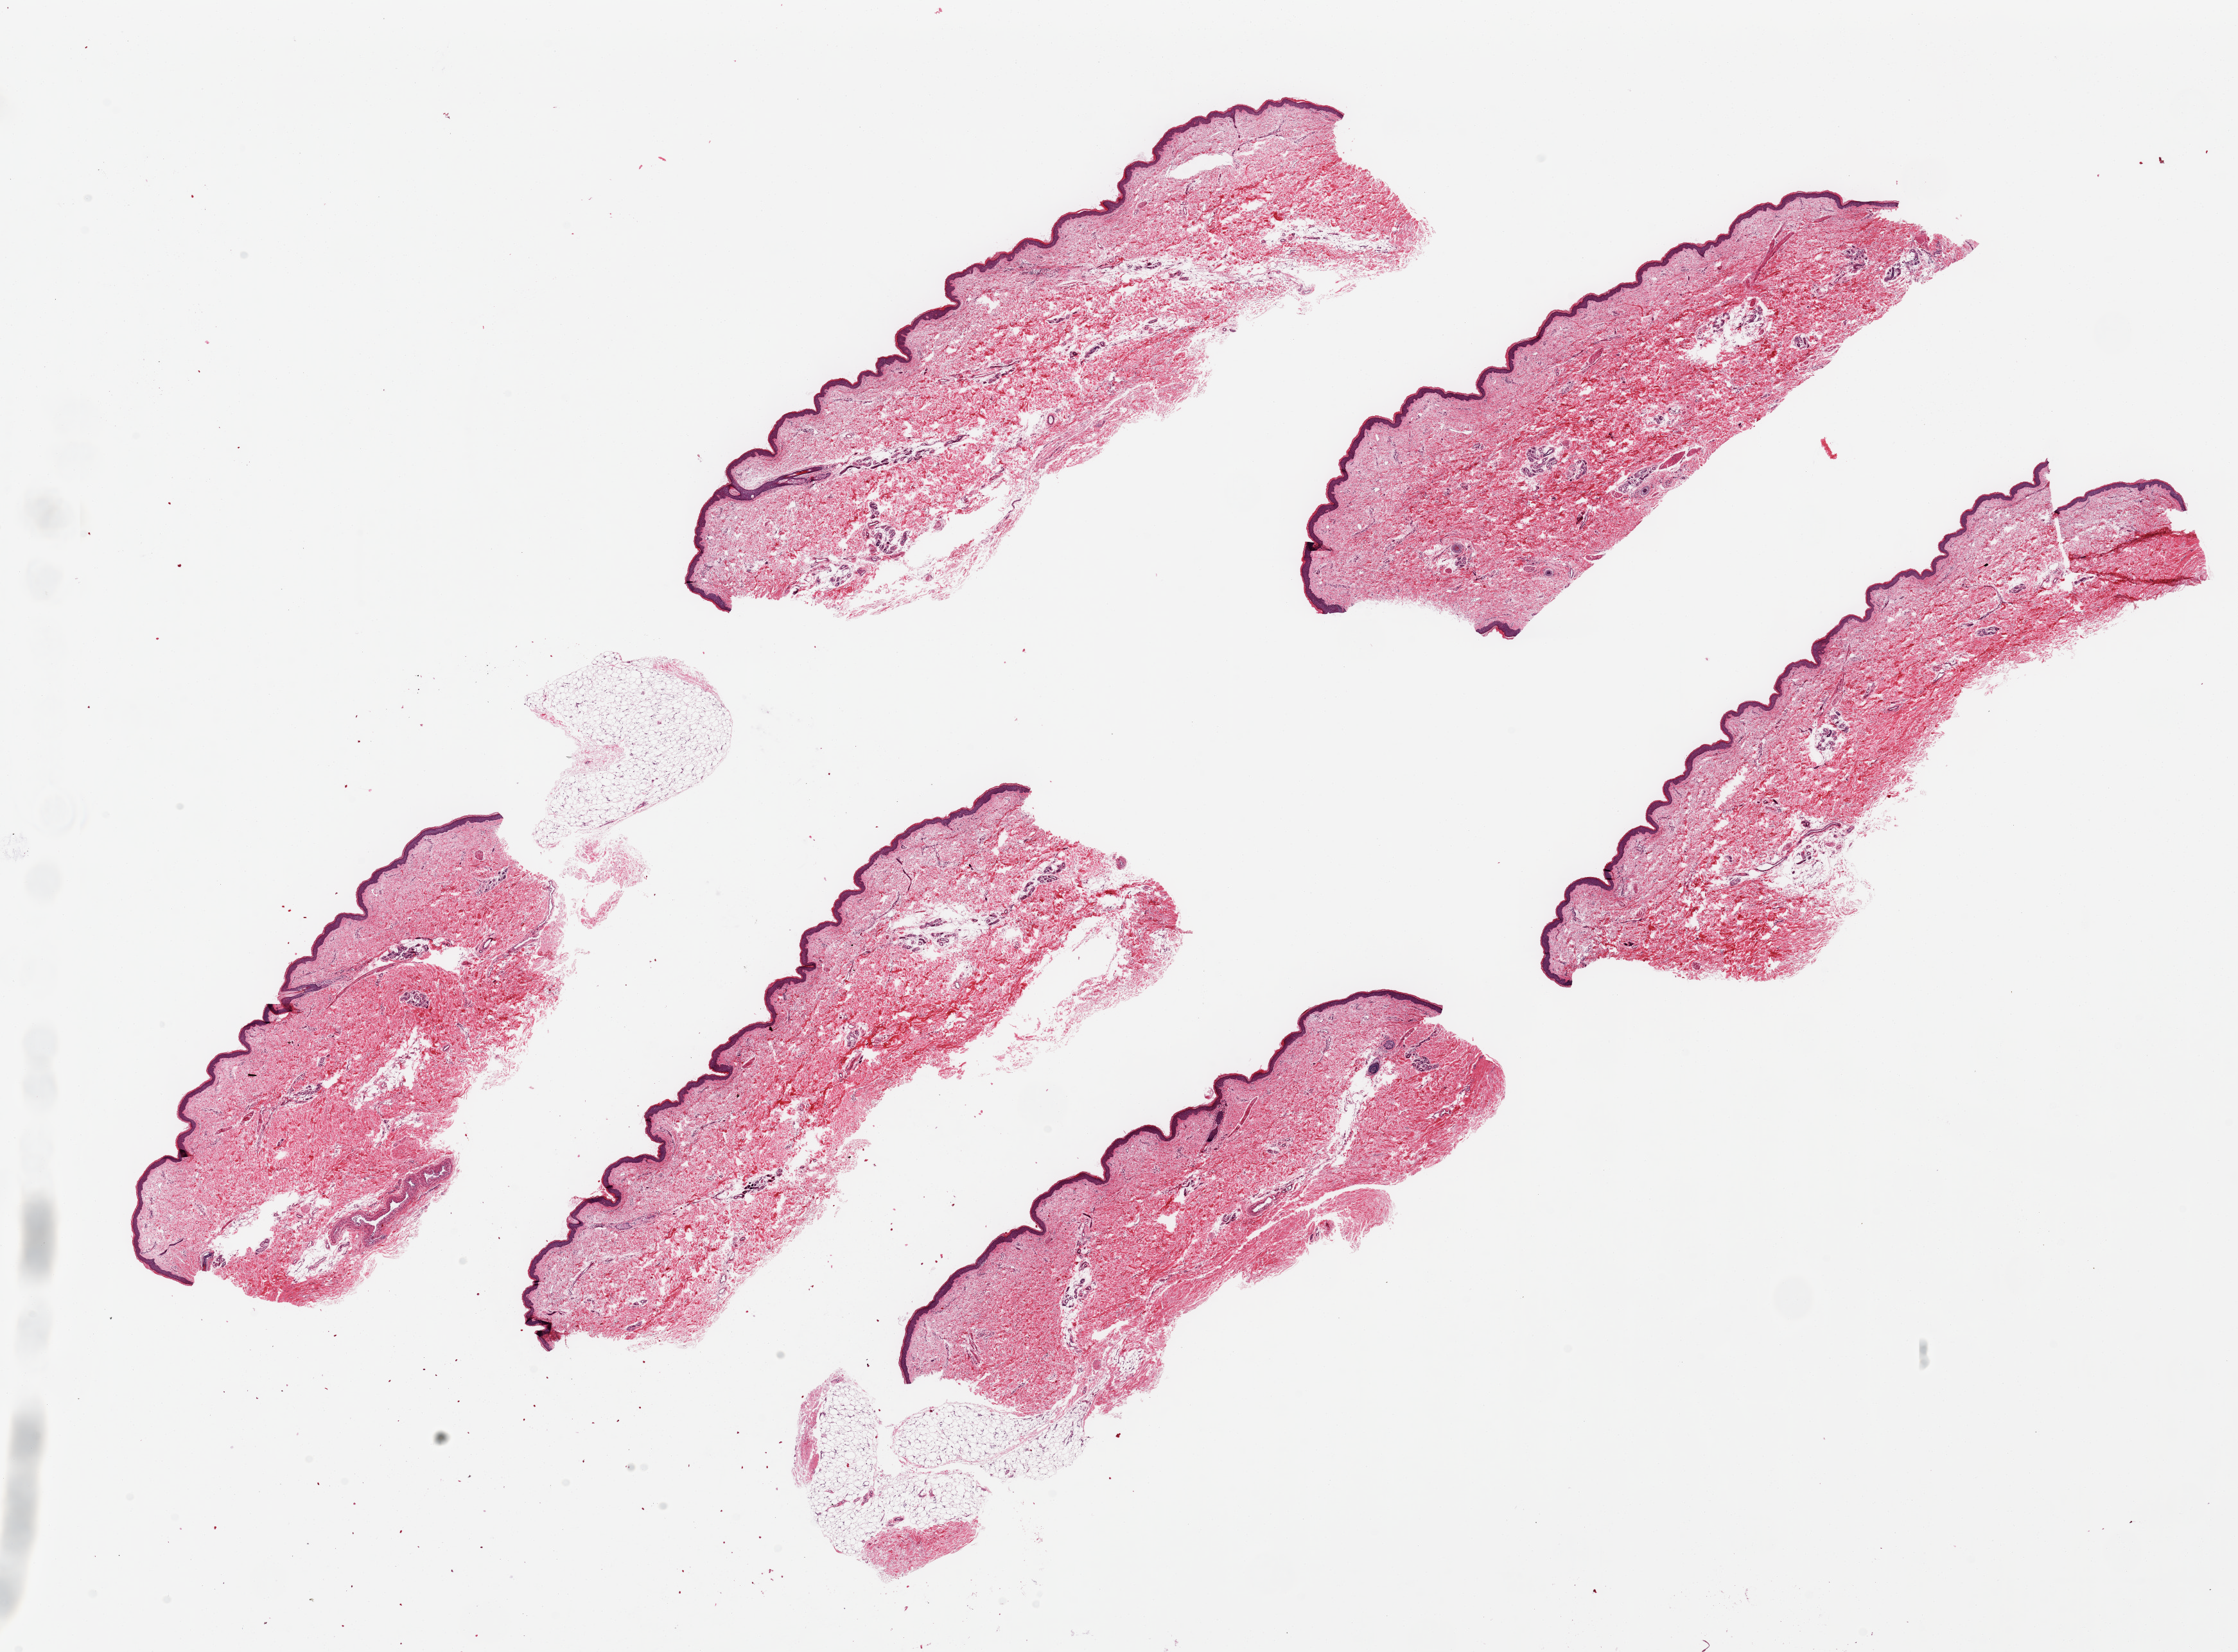
Whole-slide image, haematoxylin and eosin stain — low-resolution overview of the scanned area, about 27.6 x 20.4 mm (from a 20x scan). PAXgene-fixed, paraffin-embedded tissue. Sampled site (target tissue): skin of lower leg. Donor tissue sample. Donor: female.
Reviewer comment on this tissue sample: 6 pieces, ~8x3mm. Squamous epithelium is ~1.5-2% of thickness.